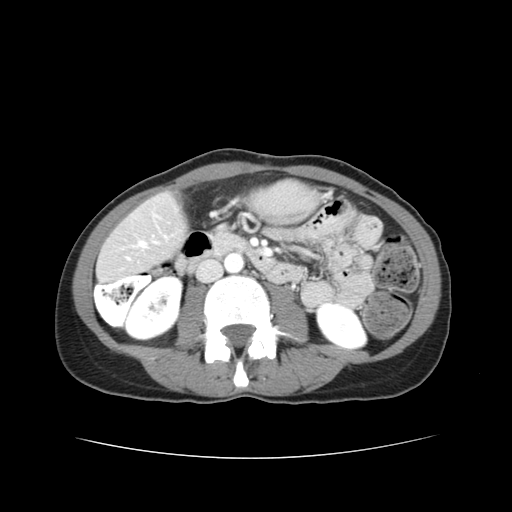
Contrast-enhanced abdominal CT, one axial slice. Position 9 of 38 along the scan axis. Reconstruction kernel STANDARD. Intravenous contrast given. Soft-tissue window (W 400 / L 40 HU). 5 mm slice thickness. 512 × 512 image matrix. Female patient, age 54 years. Case-level facts recorded for this patient, not image findings: diagnosis: colorectal cancer liver metastases, imaged before liver resection; multiple liver metastases: yes; largest metastasis: 1.1 cm; disease in both lobes: yes.
Structures marked on this image (outlined manually by an expert reader):
- hepatic veins: bounding box (x1, y1, x2, y2) in pixels: (140, 242, 146, 247)
- liver: (99, 196, 184, 279)